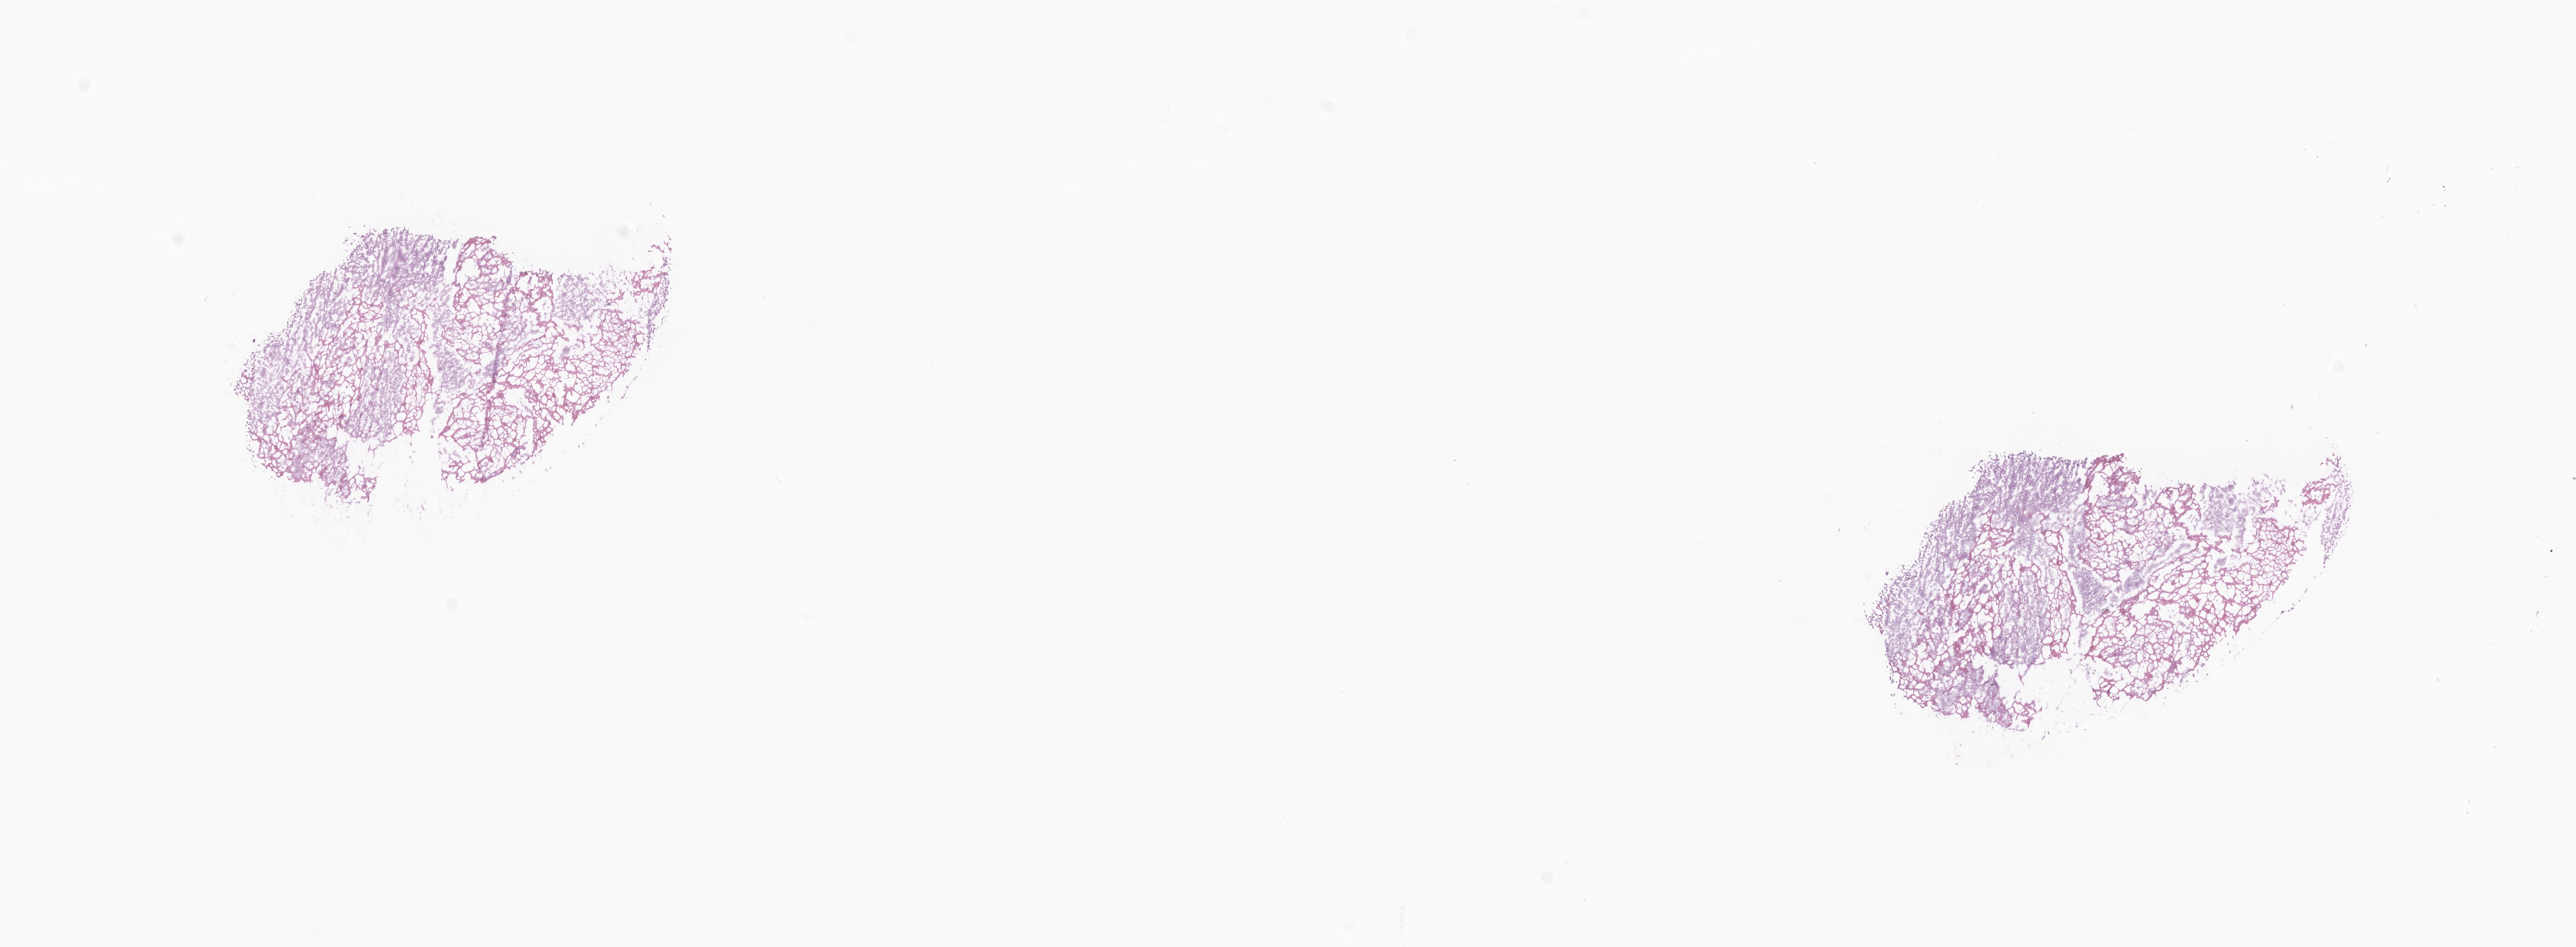
Whole-slide image, hematoxylin and eosin (H&E) stain — low-resolution overview of the scanned area, about 21.8 x 8.0 mm. Frozen section (tissue freezing medium). Specimen: metastatic tumor tissue, resected from pleura. Male patient; age at initial diagnosis 55 years.
Patient diagnosis (primary): Adenocarcinoma, NOS.